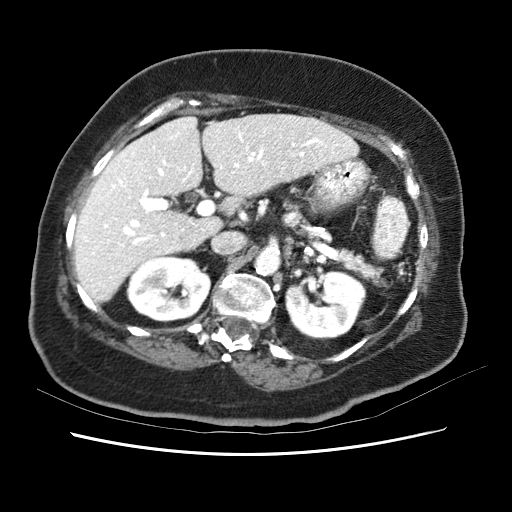
Contrast-enhanced abdominal CT (liver protocol), one axial slice; position 32 of 62 along the scan axis; reconstruction kernel STANDARD; 120 kVp; soft-tissue window (W 400 / L 40 HU); 2.5 mm slice thickness; 512 × 512 image matrix. Case-level facts recorded for this patient, not image findings: diagnosis: hepatocellular carcinoma (patient treated with transarterial chemoembolisation; whether this scan precedes or follows treatment is not stated here); TNM stage (as recorded): Stage-I; Child-Pugh class: B; tumour size: 5.3 cm.
Outlined on this slice (semi-automatically segmented with operator editing):
- liver parenchyma outside the tumour (the mass and vessels are separate outlines, so this box may not span the whole liver): bounding box (x1, y1, x2, y2) in pixels: (74, 112, 360, 303)
- liver vessels: (82, 117, 352, 289)